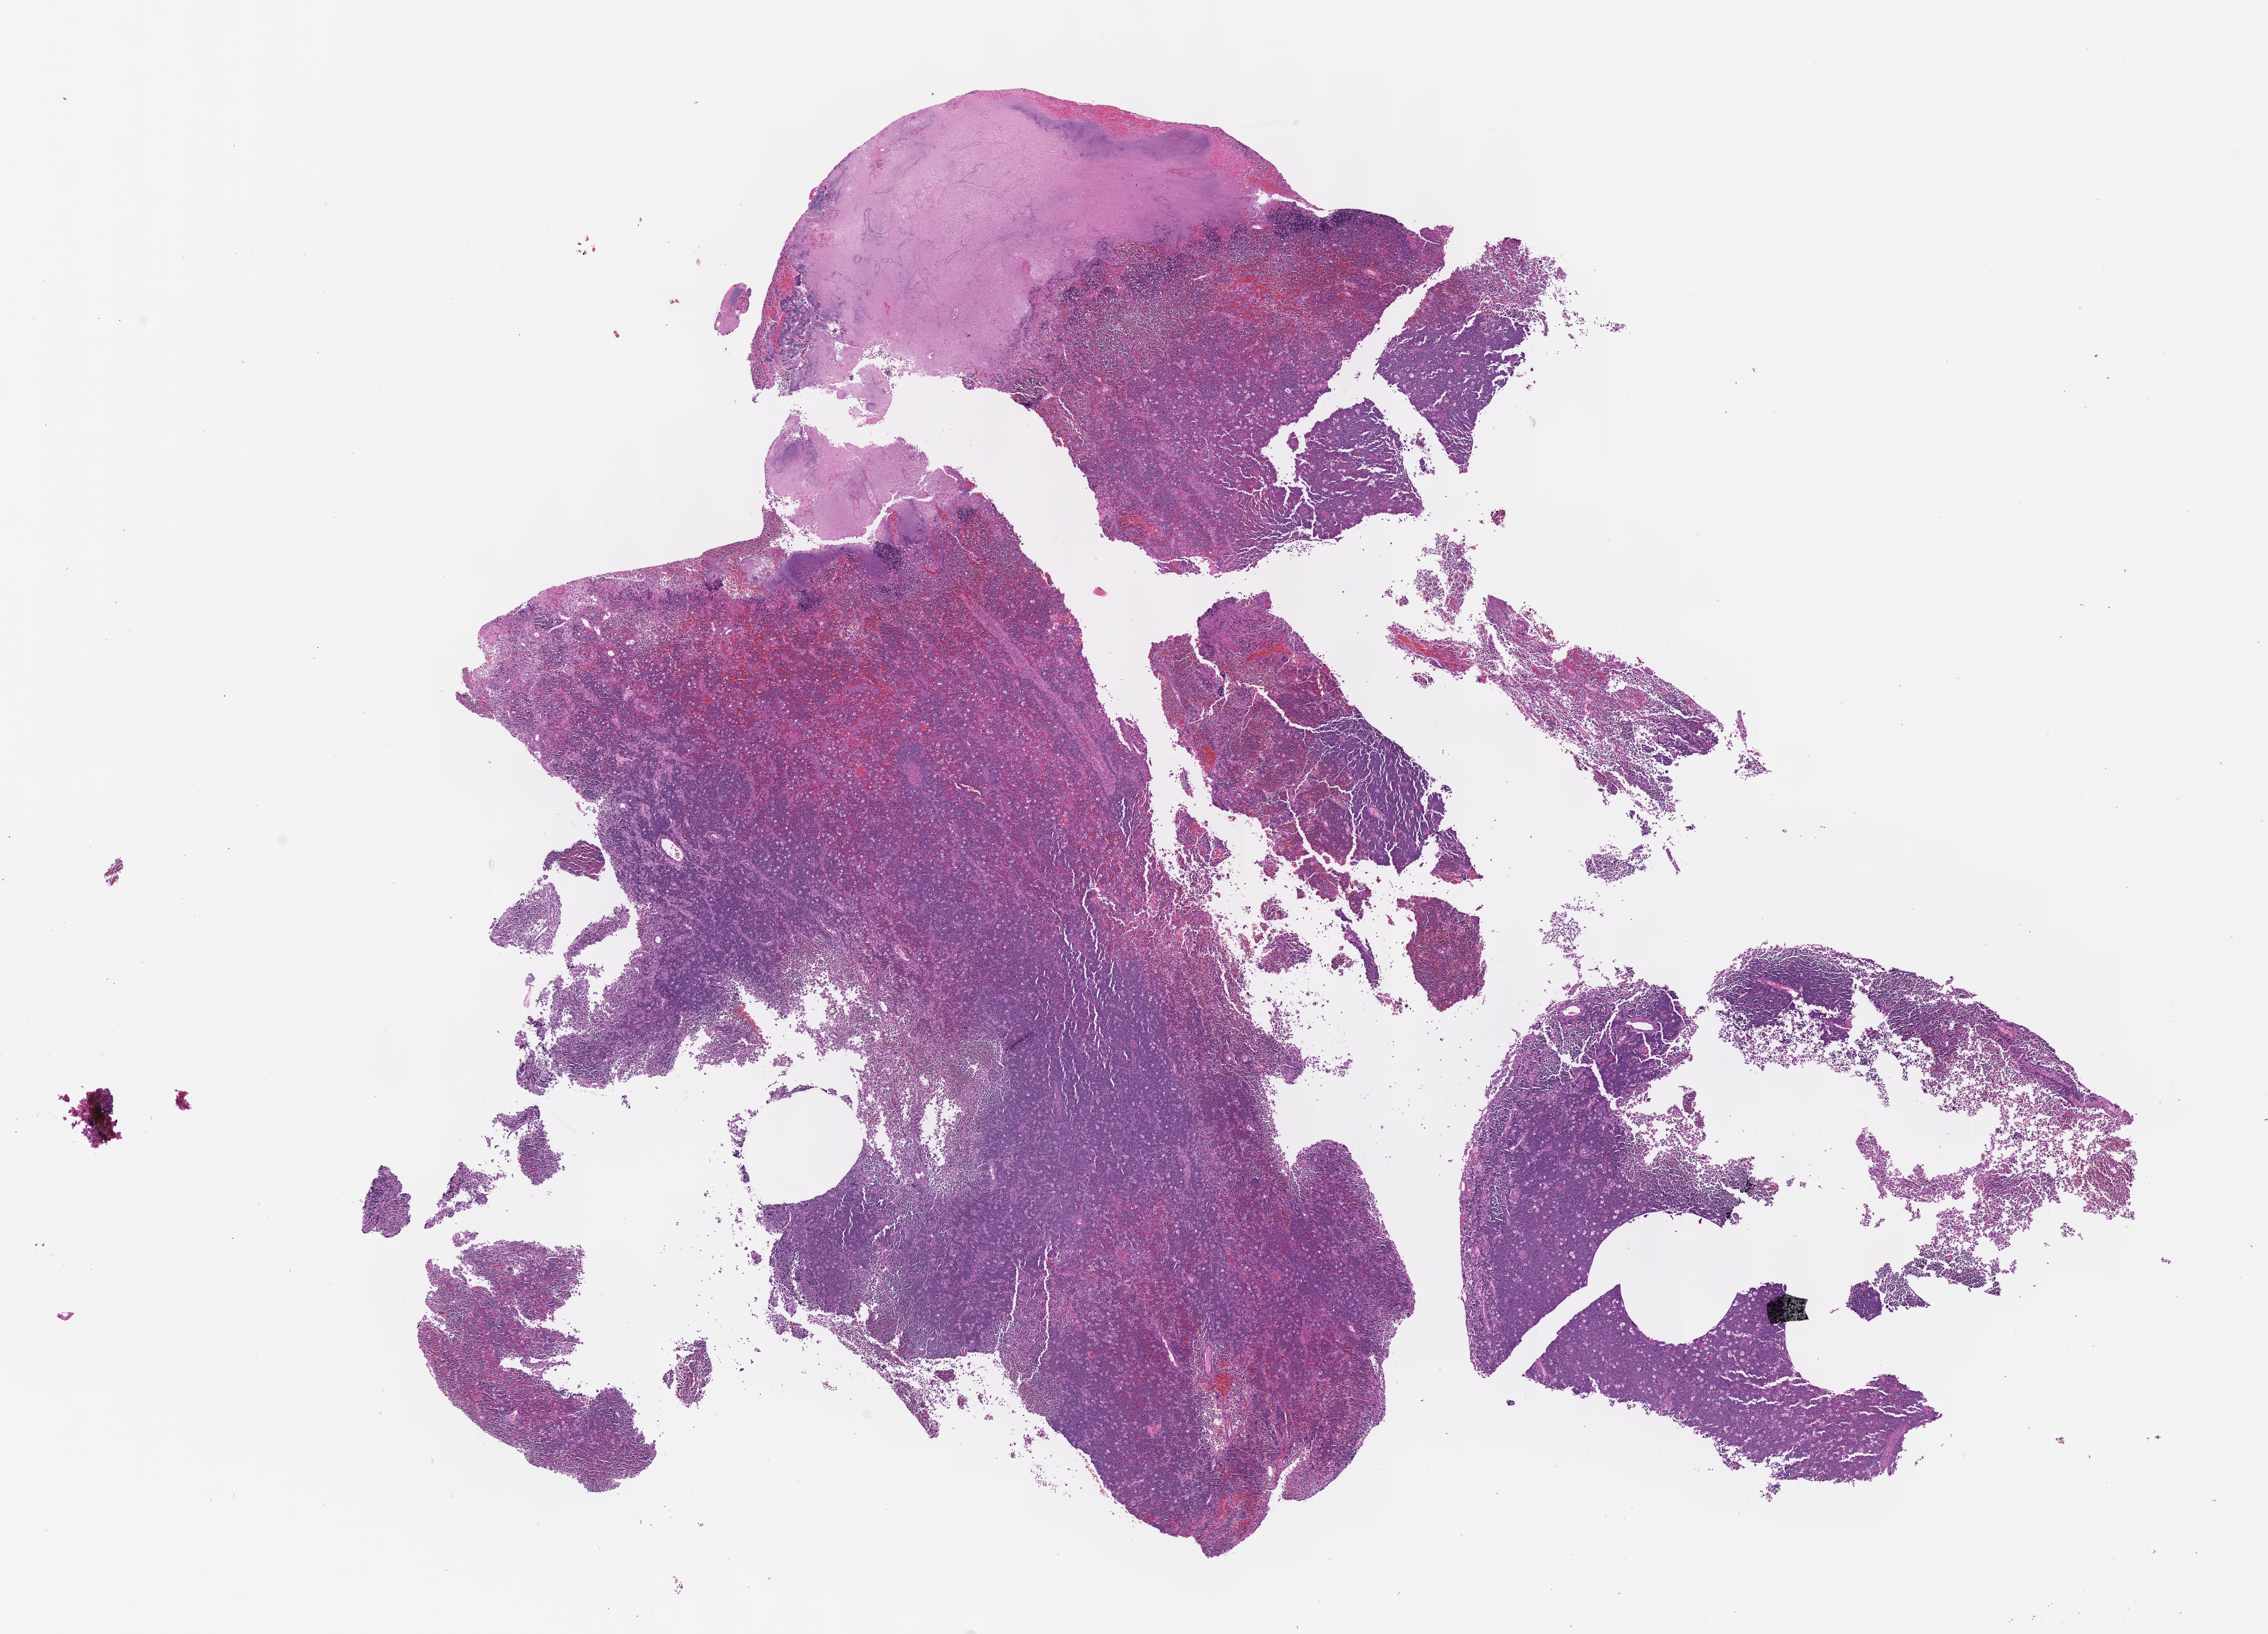
H&E whole-slide image — shown as a low-resolution overview of the whole scanned area (about 15.6 x 11.2 mm); formalin-fixed paraffin-embedded section; specimen: primary tumor; anatomic site: cranium. Female, age 5 years at initial diagnosis. Pathologist review of this section (percent, as recorded): tumor cells 70%, tumor nuclei 90%, stromal cells 5%, necrosis 20%, normal cells 5%. Infiltration values recorded for this section: lymphocyte infiltration 40%, monocyte infiltration 30%, neutrophil infiltration 15%.
Ann Arbor stage (patient): Stage I. Section: bottom of the tissue portion. Diagnosis: Burkitt lymphoma, NOS.